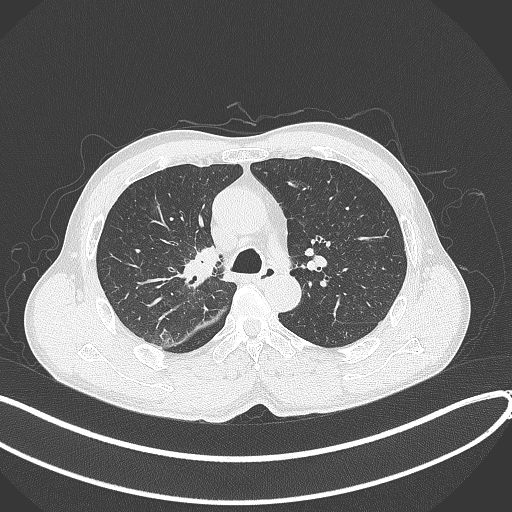
Chest CT, one axial slice. Slice 262 of 409 in the series (ordered by position). Reconstruction kernel B70f. 120 kVp. Lung window (W 1500 / L -600 HU). 1 mm slice thickness. 512 × 512 image matrix, field of view 400 × 400 mm. Male patient, age 53 years. From the clinical record (not read from this slice): clinical TNM (as recorded): T1b N0 M0.
Structures marked on this image (rectangle marked by the reading radiologist):
- lung tumour (recorded histology: squamous cell carcinoma): bounding box [x1, y1, x2, y2] px = [173, 241, 223, 289]